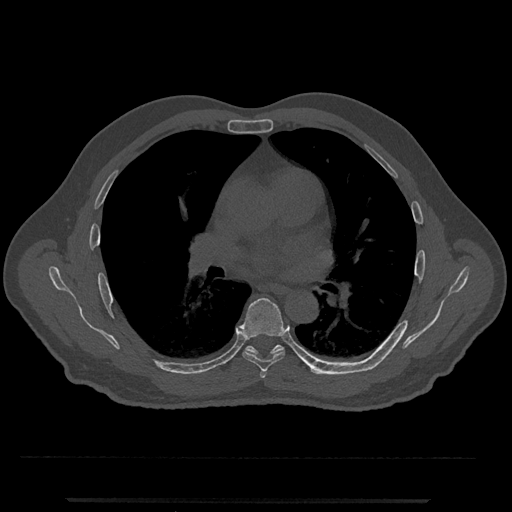
CT including the spine, one axial slice. Slice 722 of 797 in the series (ordered by position). Reconstruction kernel Br40s/3. Bone window (W 1800 / L 400 HU). 0.5 mm slice thickness. 512 × 512 image matrix. Male patient, age 63 years. Case-level facts recorded for this patient, not image findings: primary cancer: prostate.
Outlined on this slice (semi-automatic segmentation, software-assisted and operator-edited):
- T5 vertebra: box from (x=260, y=371) to (x=267, y=378) px
- T6 vertebra: (x=239, y=298)–(x=285, y=372)
- T7 vertebra: (x=245, y=344)–(x=330, y=375)